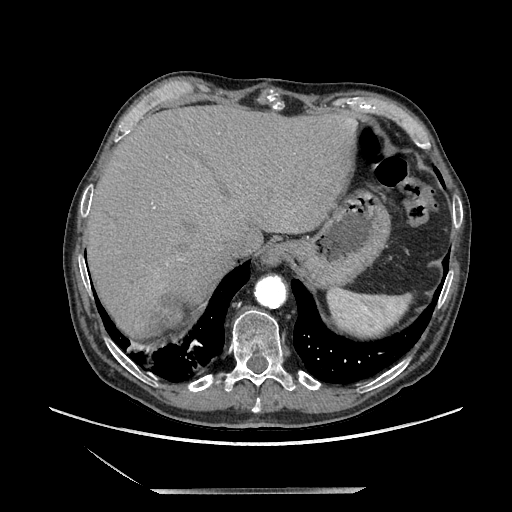
Contrast-enhanced abdominal CT, one axial slice. Slice 178 of 243 in the series (ordered by position). Soft-tissue window (W 400 / L 40 HU). 1.25 mm slice thickness. 512 × 512 image matrix, field of view 420 × 420 mm. Male patient. From the clinical record (not read from this slice): diagnosis: adrenocortical carcinoma; tumour side: right adrenal; tumour size at pathology: 16 cm; Ki-67 index: 17 %; stage (as recorded): 3.
Structures marked on this image (semi-automatic segmentation, software-assisted and operator-edited):
- mass: bounding box (x1, y1, x2, y2) in pixels: (132, 294, 189, 337)